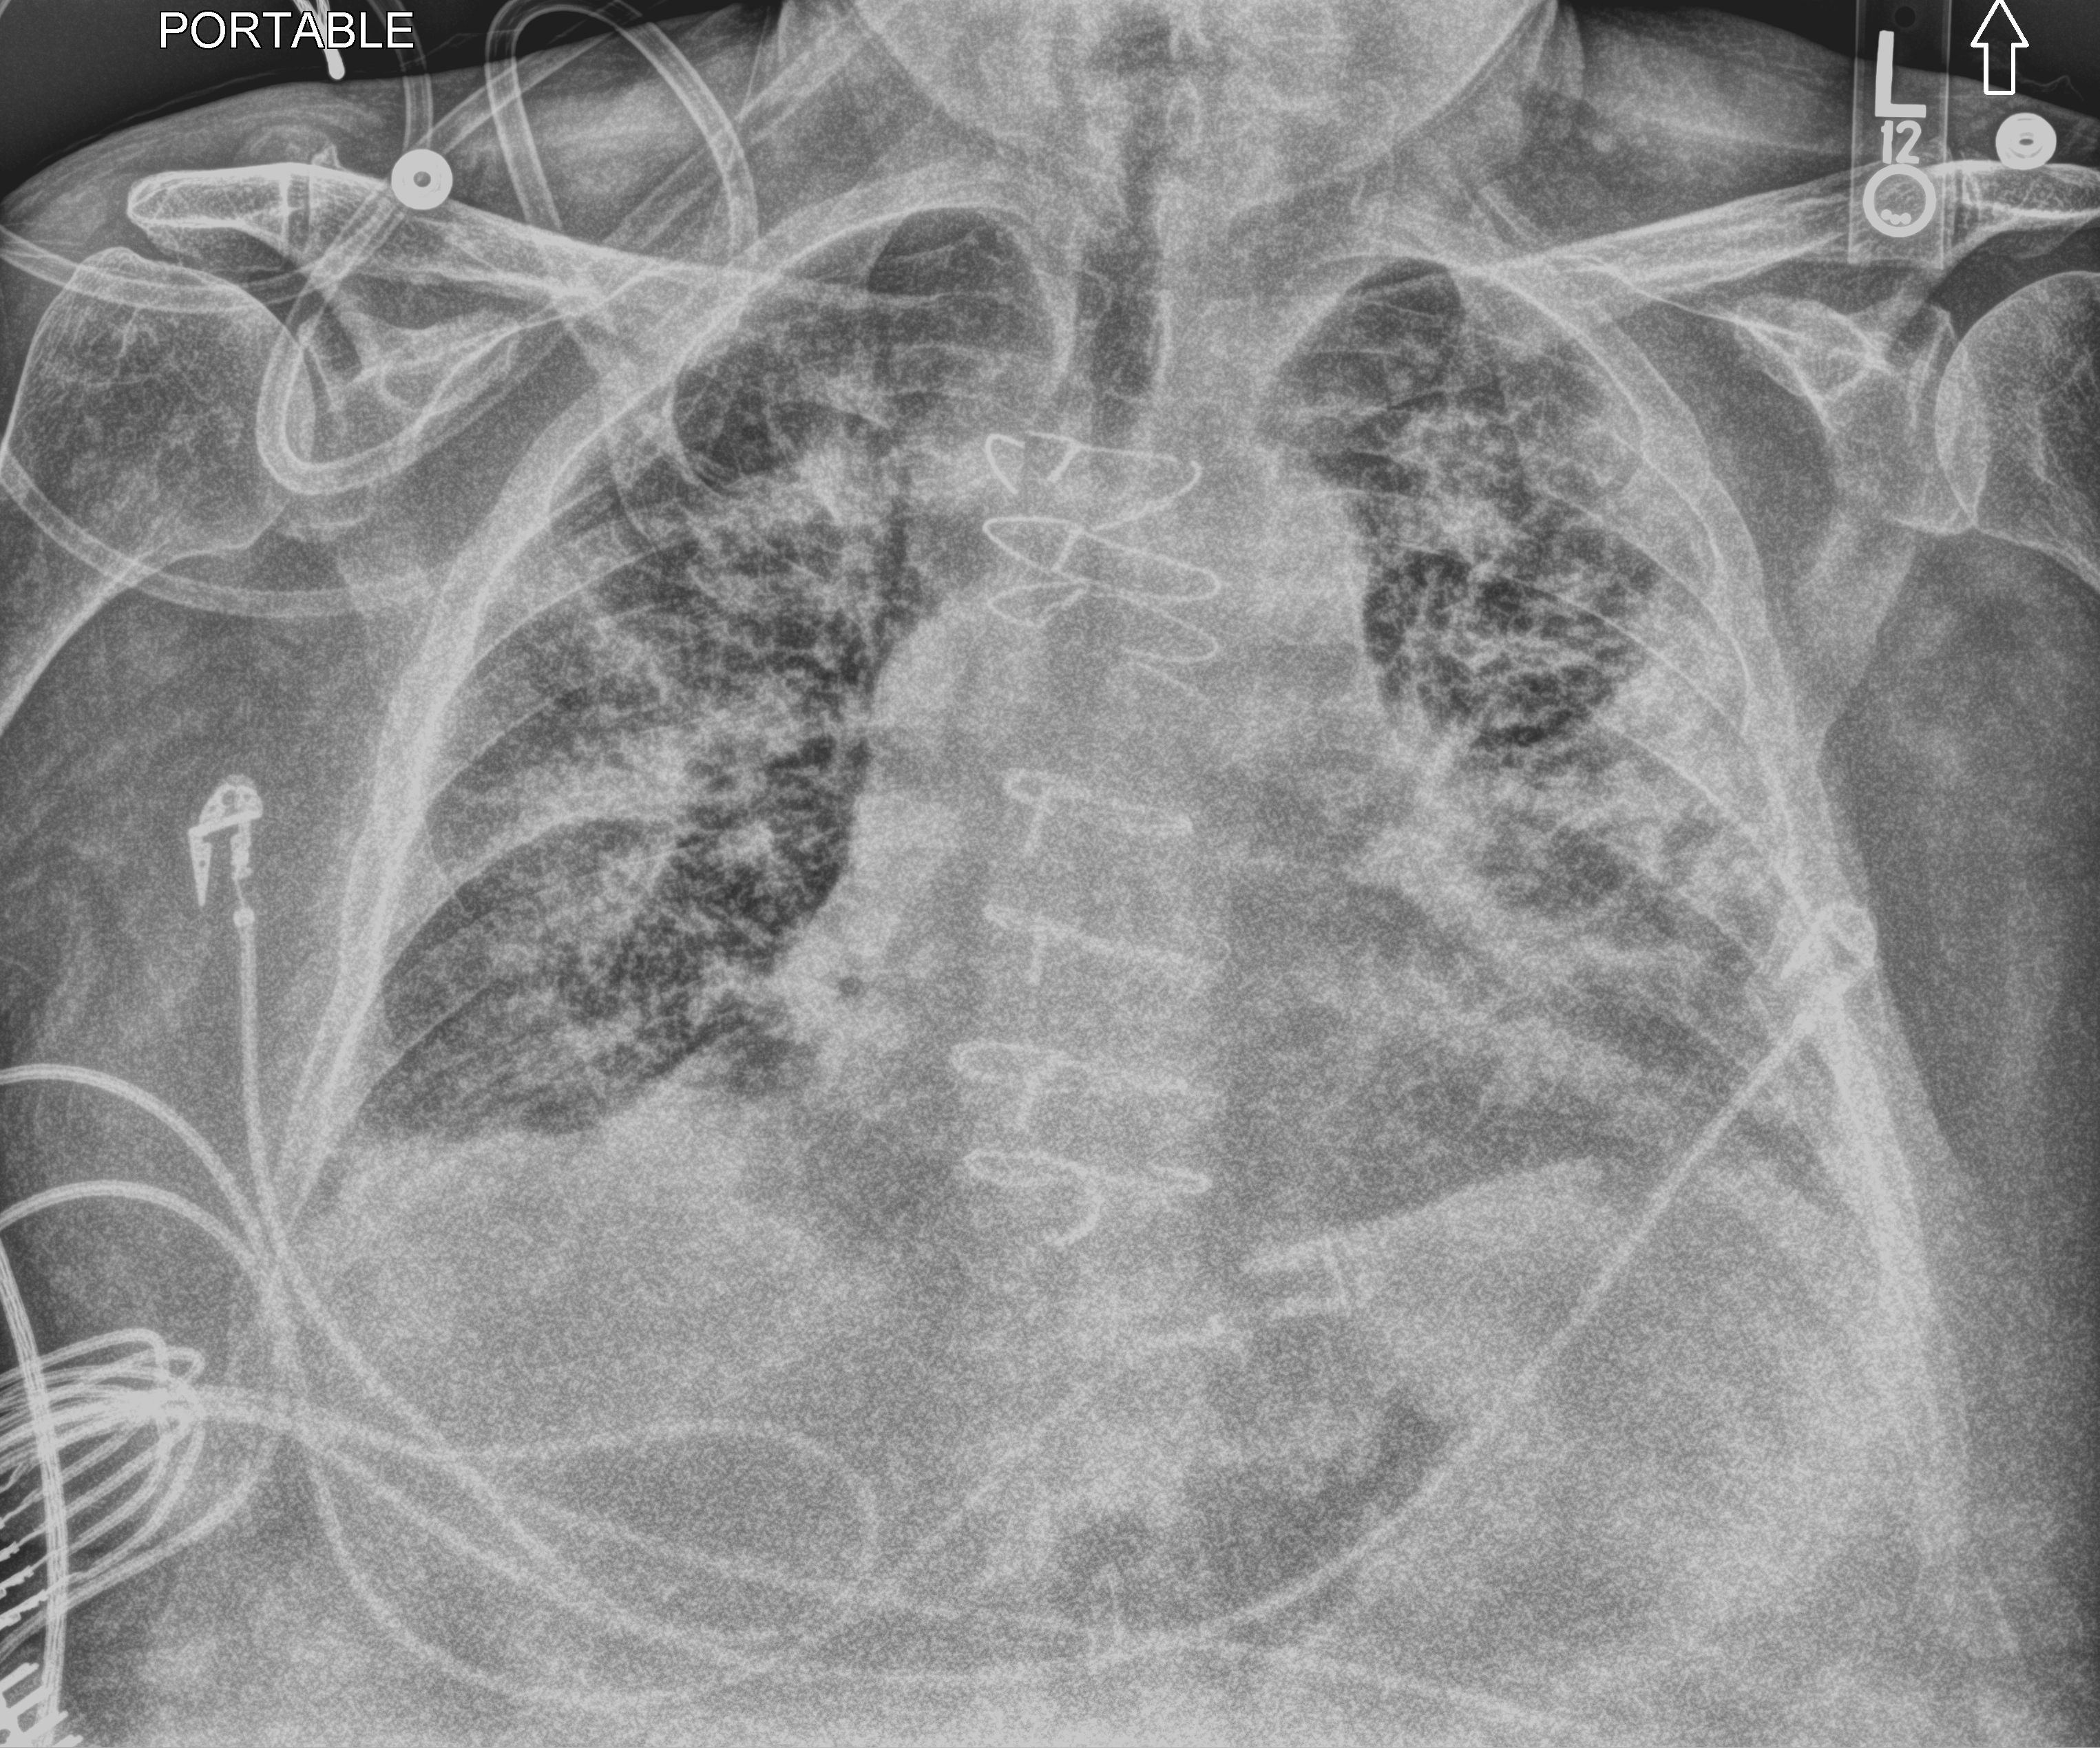
Chest X-ray (portable), anteroposterior (AP) projection. Male patient hospitalised with COVID-19, age 75–90 years.
From the hospital-stay record, not from the radiograph (when in the stay this image was taken is not recorded):
- admitted to intensive care during this hospital stay: no